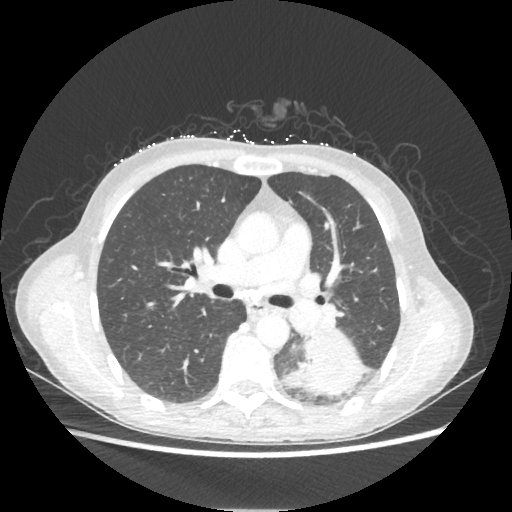
Chest CT, one axial slice; position 131 of 221 along the scan axis; 80 kVp; lung window (W 1500 / L -600 HU); 1.25 mm slice thickness; 512 × 512 image matrix. Patient: female, 53 years. From the clinical record (not read from this slice): clinical TNM (as recorded): T3 N0 M0.
Annotated regions visible in this slice (bounding box drawn by a radiologist):
- lung tumour (recorded histology: adenocarcinoma): bounding box <285,332,367,396> (left, top, right, bottom; pixels)